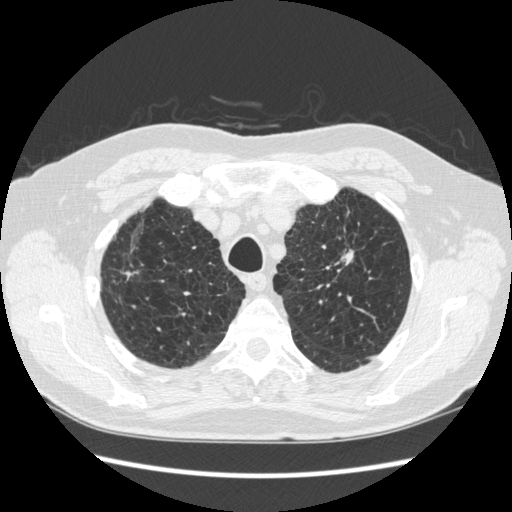
Axial slice from a low-dose chest CT screening exam. Third screening round (two years after baseline). Lung window (W 1500 / L -600 HU). 1.25 mm slice thickness. Slice 49 of 267 in the series. 512 × 512 image matrix, field of view 360 × 360 mm. Male, age 70 years at enrolment. Former smoker at enrolment.
Expert-annotated lung lesion, bounding box (x1, y1, x2, y2) in pixels: (323, 214, 373, 279). The screening reader recorded 2 non-calcified nodules or masses ≥4 mm on this exam (left upper lobe, right lower lobe); which of them this box marks is not recorded. Lung cancer was diagnosed 92 days after this screen: squamous cell carcinoma, NOS, left upper lobe, moderately differentiated (G2), stage IA (AJCC 6th edition), 18 mm at pathology.